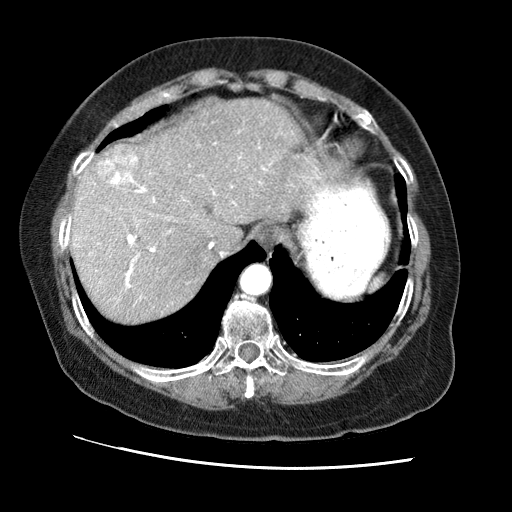
Contrast-enhanced abdominal CT (liver protocol), one axial slice; reconstruction kernel STANDARD; 120 kVp; soft-tissue window (W 400 / L 40 HU); 2.5 mm slice thickness; 512 × 512 image matrix, field of view 340 × 340 mm. Case-level facts recorded for this patient, not image findings: diagnosis: hepatocellular carcinoma (patient treated with transarterial chemoembolisation; whether this scan precedes or follows treatment is not stated here); TNM stage (as recorded): Stage-II; Child-Pugh class: A; tumour differentiation: no biopsy.
Annotated regions visible in this slice (semi-automatic segmentation, software-assisted and operator-edited):
- abdominal aorta: bounding box (x1, y1, x2, y2) in pixels: (242, 265, 271, 294)
- liver parenchyma outside the tumour (the mass and vessels are separate outlines, so this box may not span the whole liver): (70, 98, 328, 322)
- mass: (94, 147, 137, 185)
- liver vessels: (74, 142, 320, 299)